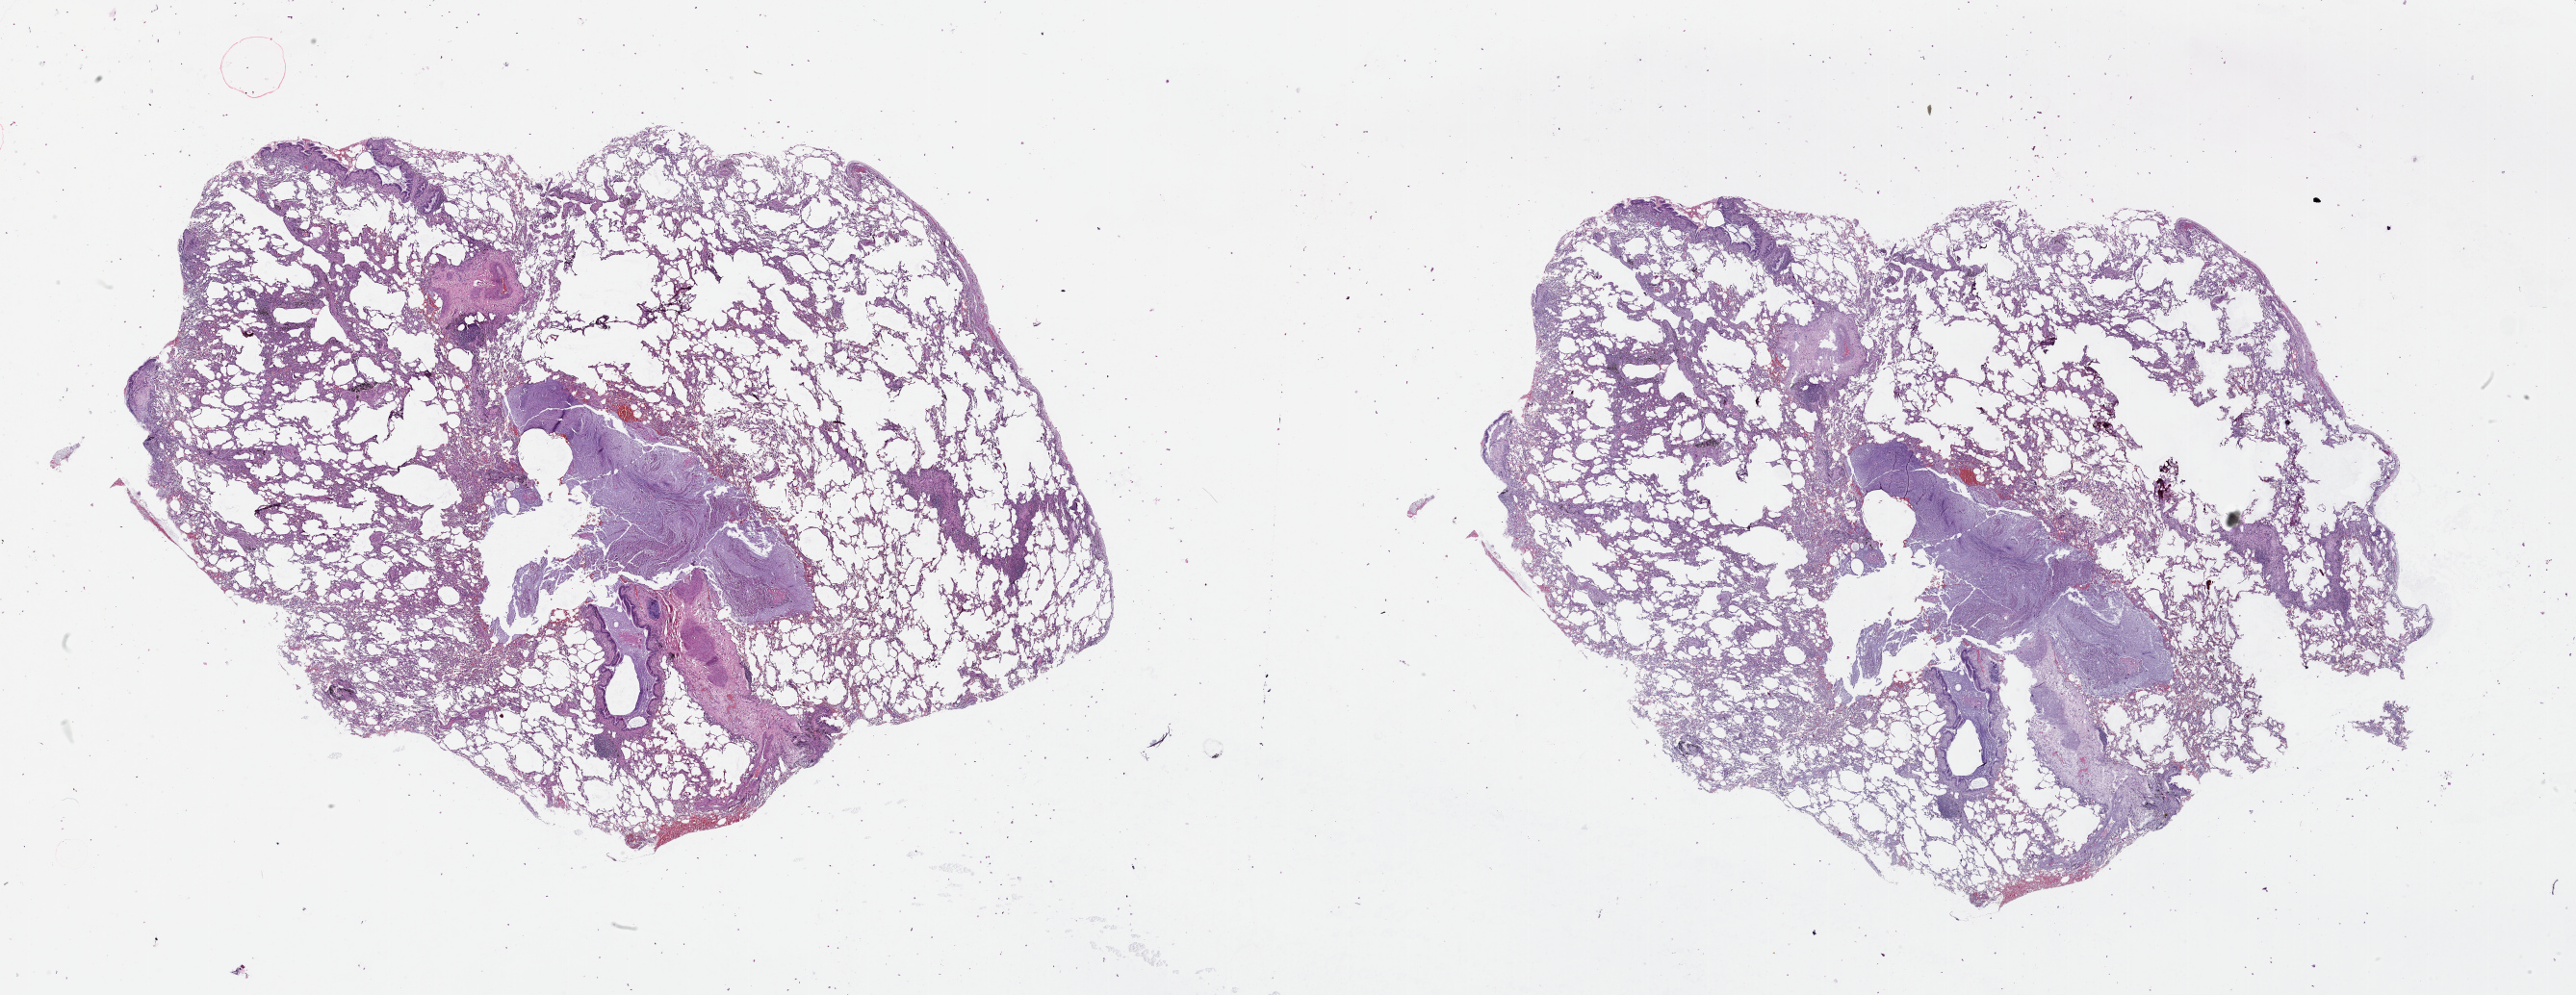
H&E whole-slide image, low-resolution overview of the scanned area, about 43.1 x 16.7 mm. Lung, tissue type not recorded.
Patient diagnosis (cohort enrolment): squamous cell carcinoma (lung).